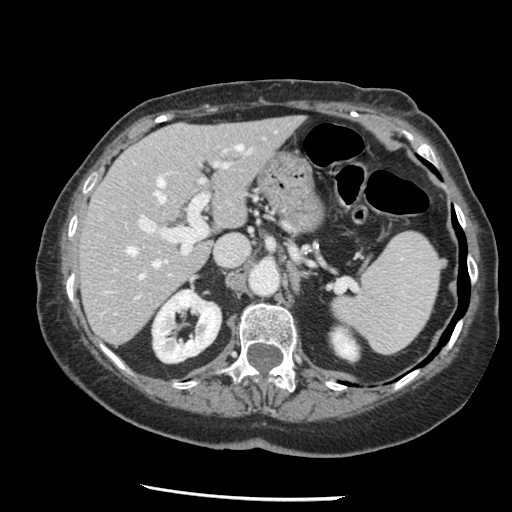
Contrast-enhanced abdominal CT, one axial slice; position 85 of 148 along the scan axis; reconstruction kernel STANDARD; intravenous contrast given; soft-tissue window (W 400 / L 40 HU); 512 × 512 image matrix, field of view 330 × 330 mm. Female patient, age 85 years. From the clinical record (not read from this slice): diagnosis: colorectal cancer liver metastases, imaged before liver resection; multiple liver metastases: no; largest metastasis: 0.9 cm; disease in both lobes: no.
Outlined on this slice (manually delineated by an expert):
- hepatic veins: bounding box <127,146,242,279> (left, top, right, bottom; pixels)
- liver: <81,118,300,344>
- planned liver remnant (the part of the liver to remain after resection): <81,118,300,344>
- portal vein (with intrahepatic branches): <141,148,230,253>